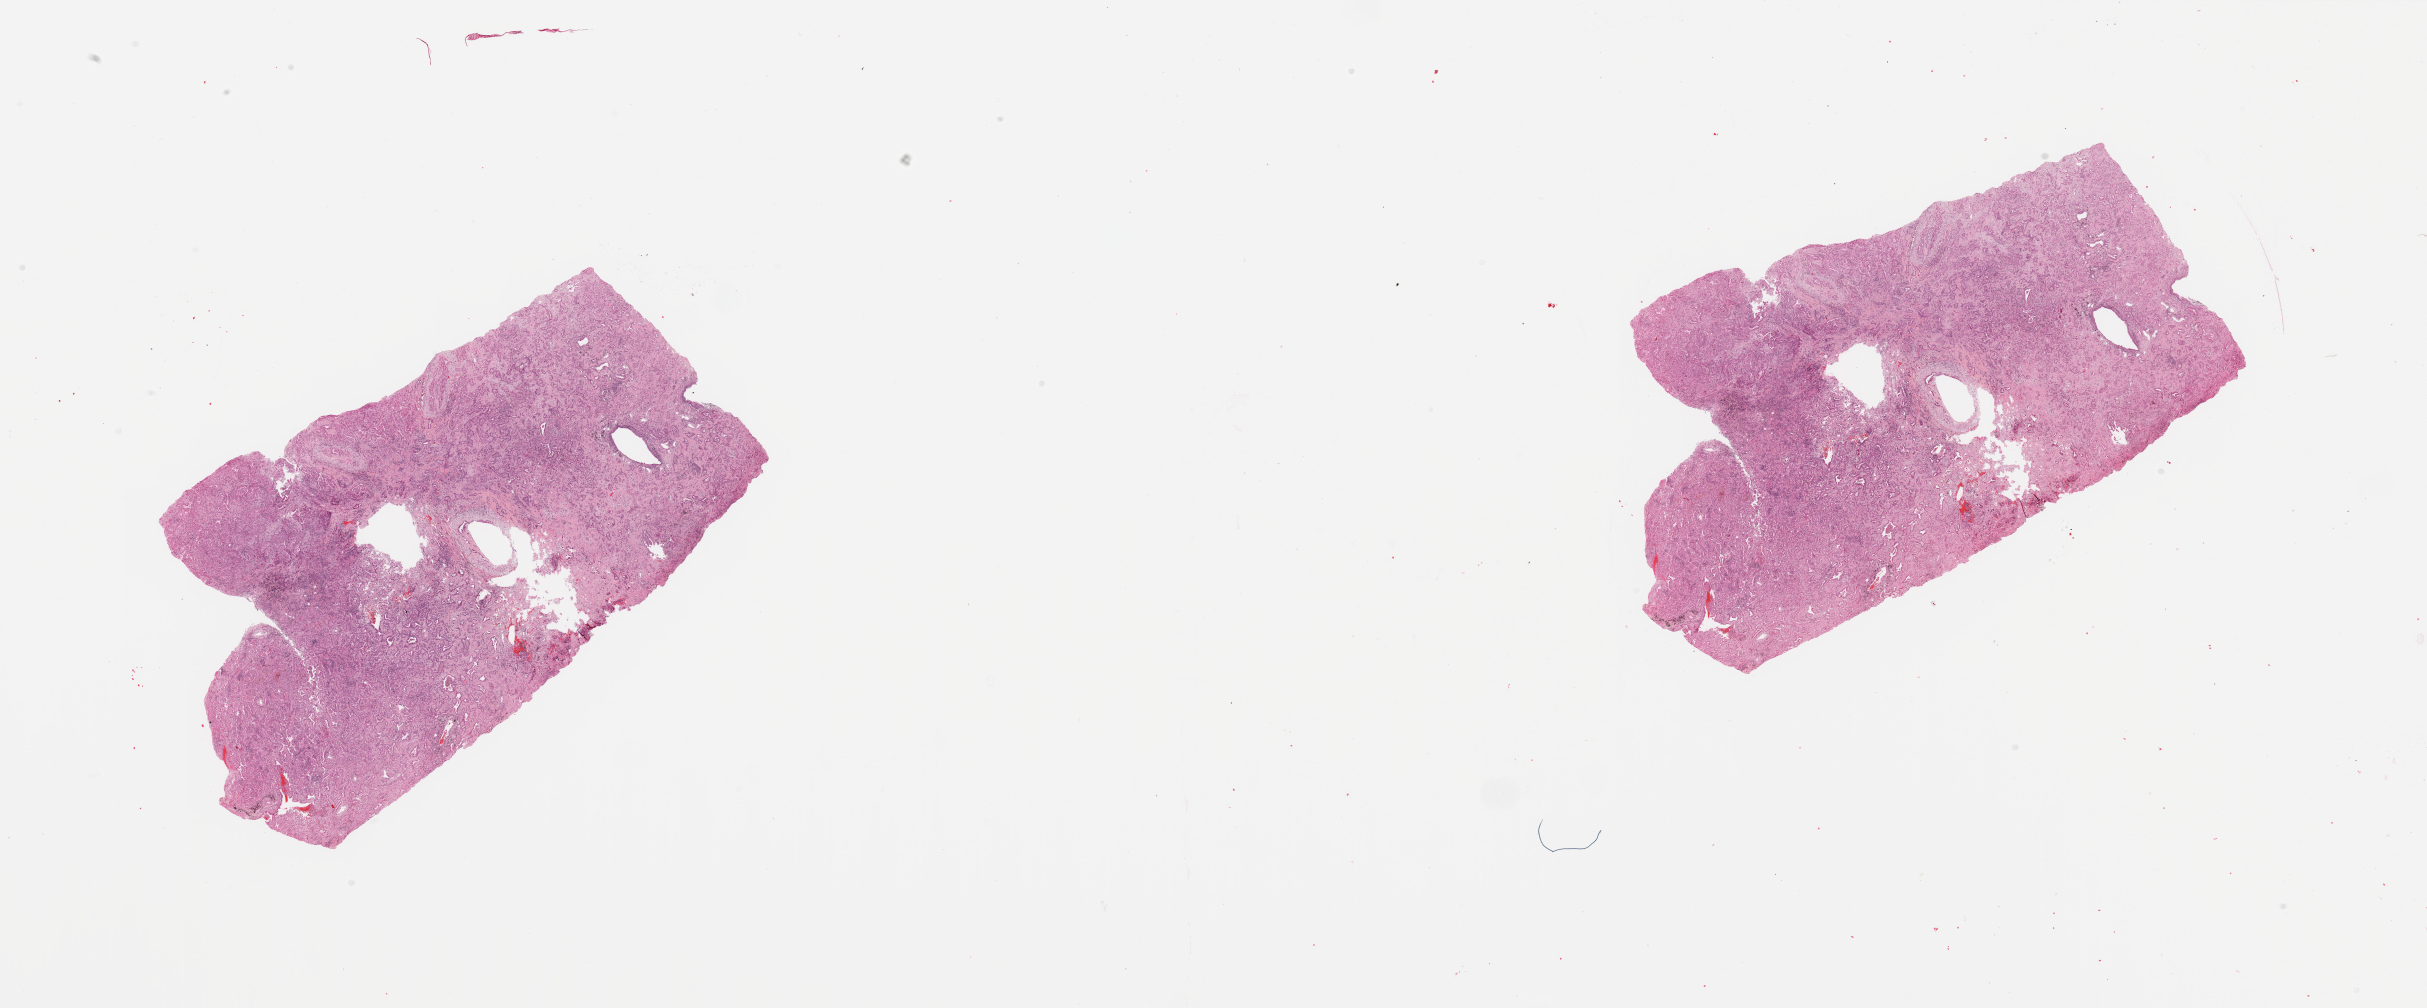
Digitized H&E-stained tissue section (whole slide), shown as a low-resolution overview of the whole scanned area (about 38.4 x 15.9 mm); tumour tissue sample, sampled site: lung. Female, 69 y/o. Histologic grade: G2 (moderately differentiated). Pathologist review of this section (percent, as recorded): tumour nuclei 65%, necrosis 5%.
Primary tumour site (as recorded): right upper lobe. Diagnosis: Adenocarcinoma, NOS. AJCC pathologic stage: IB.